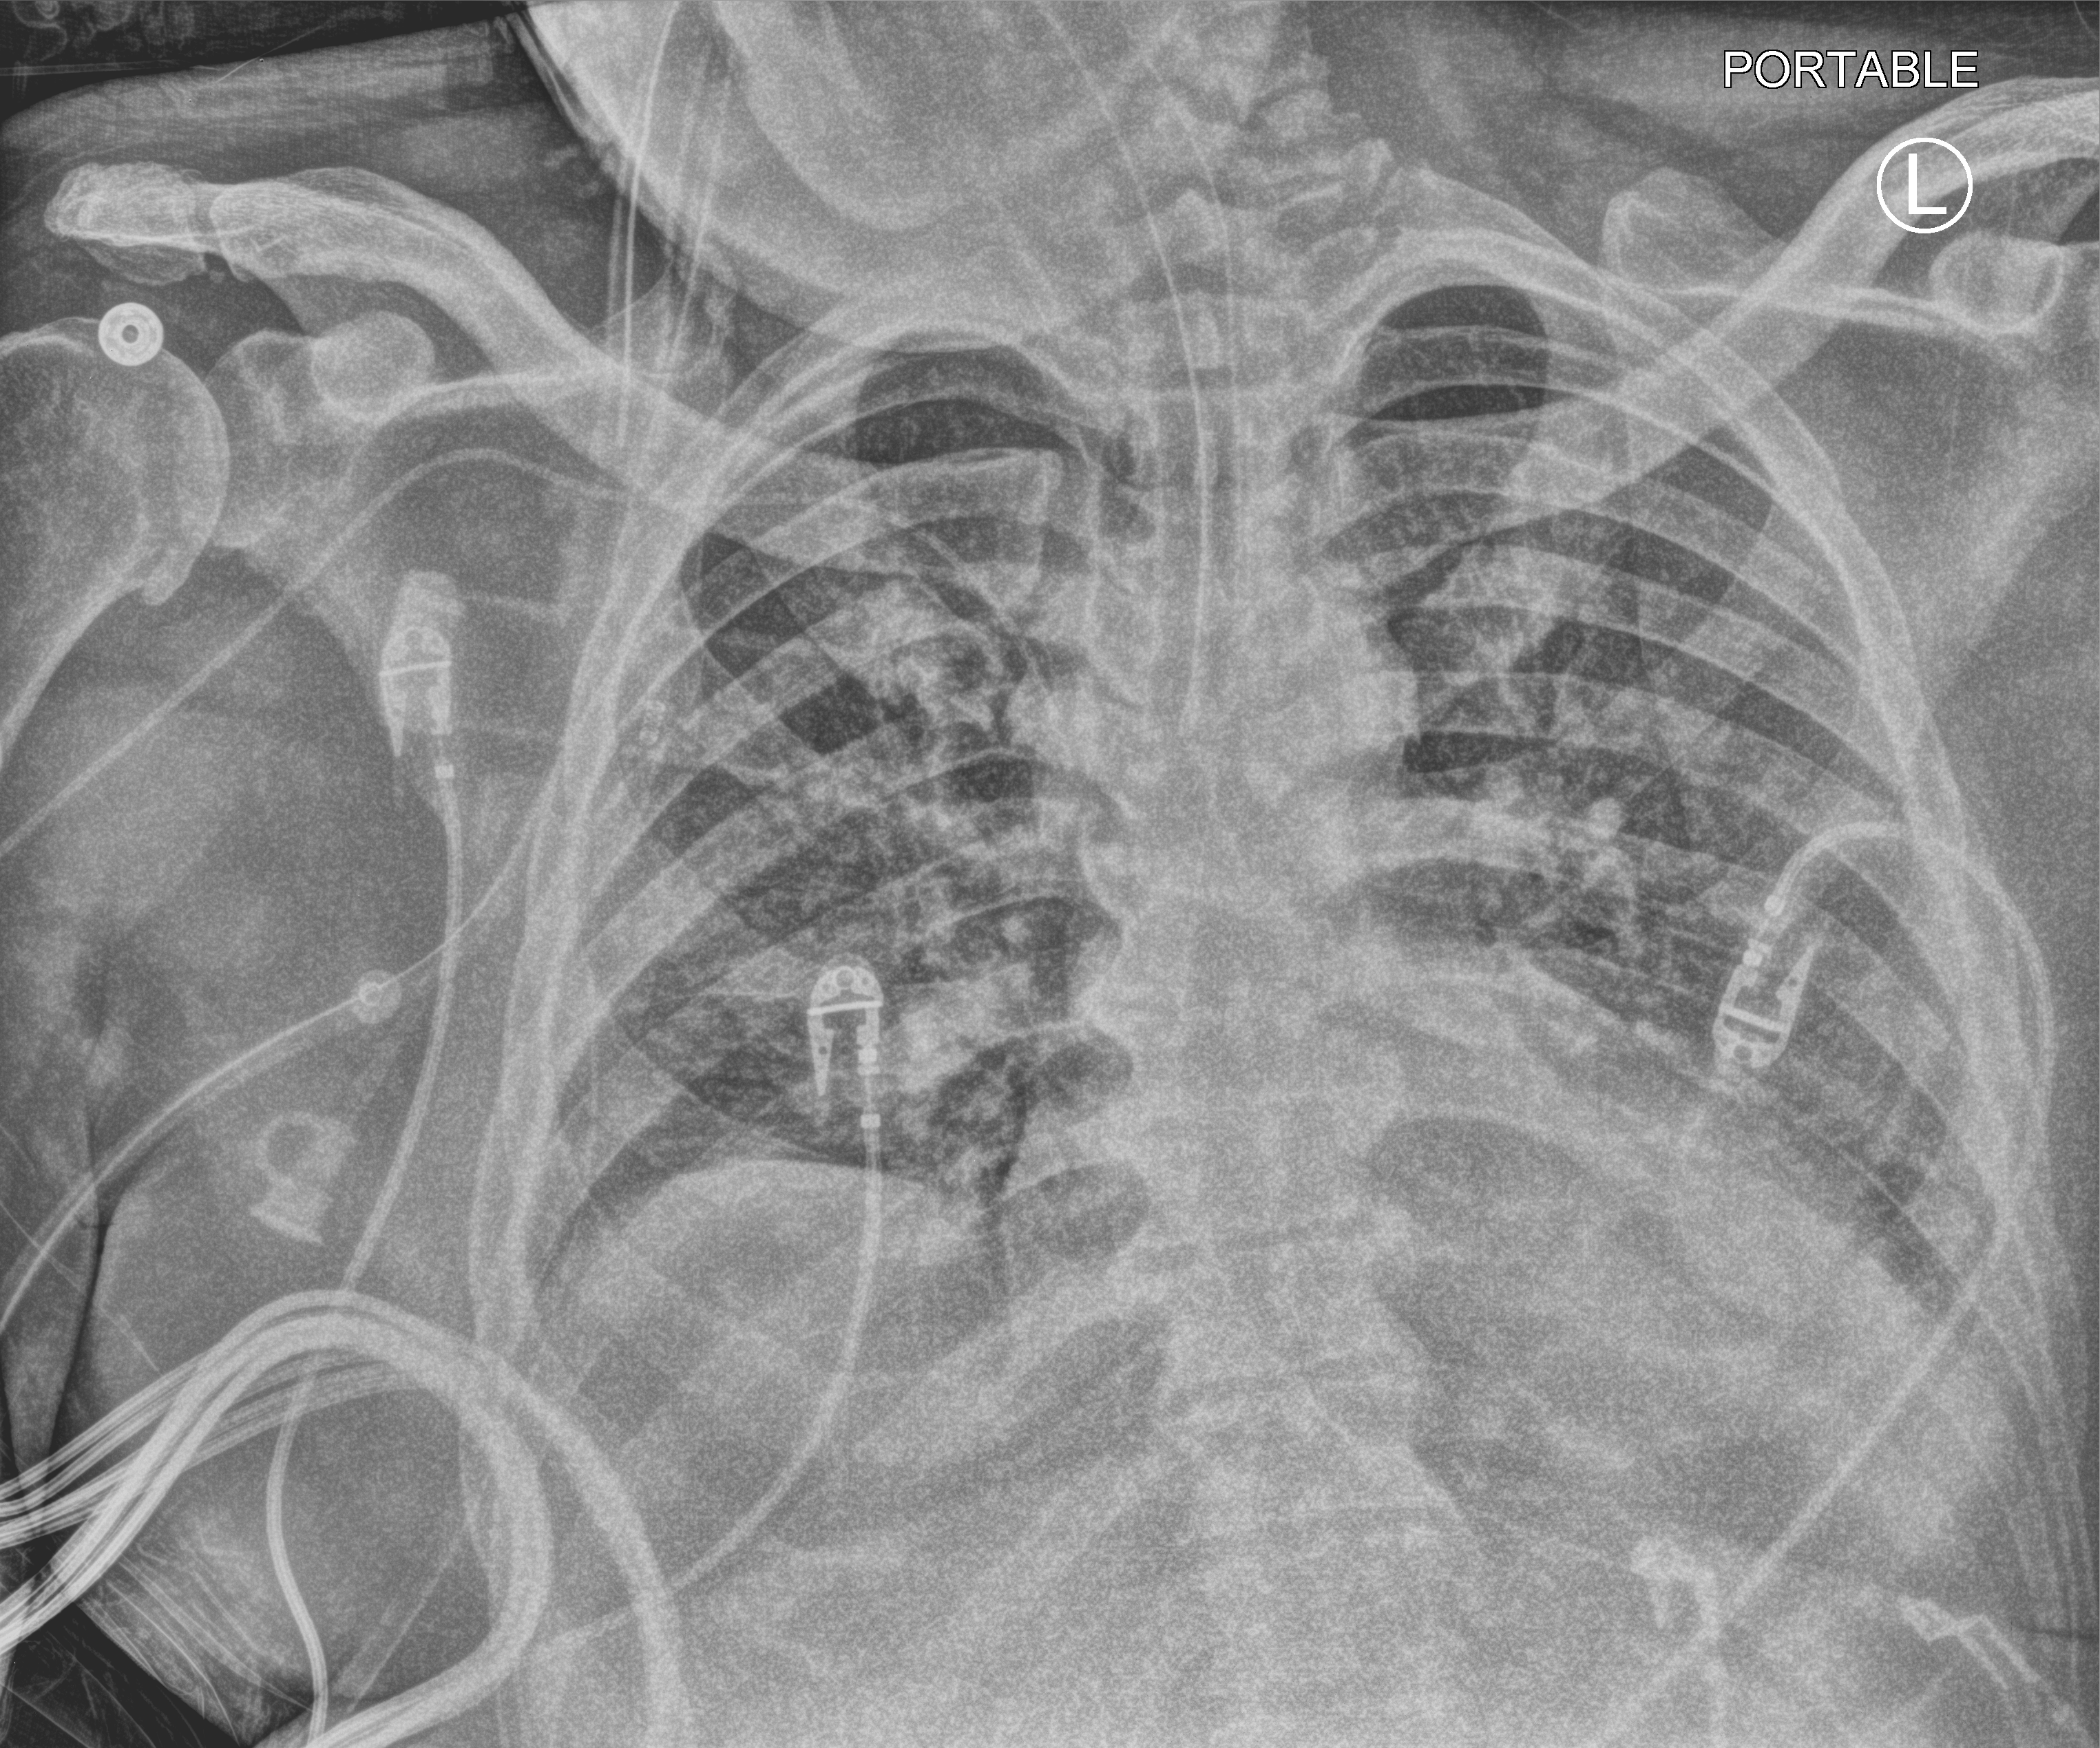
Chest X-ray (portable); anteroposterior (AP) projection. Male patient hospitalised with COVID-19, age 18–59 years.
Admission-level facts for this patient (not findings on this image; timing relative to this image not recorded): mechanically ventilated during this hospital stay: yes; admitted to intensive care during this hospital stay: yes; chronic kidney disease (admission record): no.